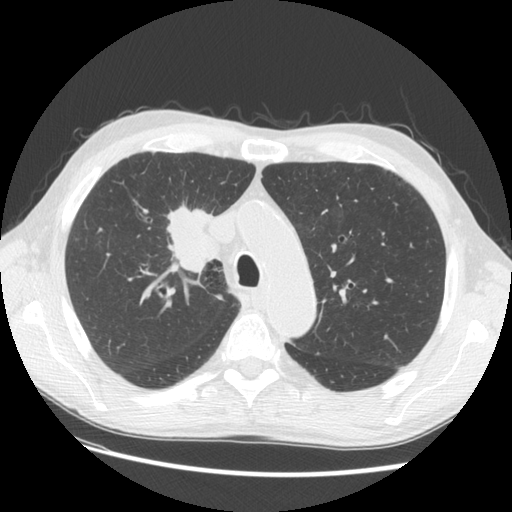
Axial slice from a low-dose chest CT screening exam; third screening round (two years after baseline); lung window (W 1500 / L -600 HU); 2.5 mm slice thickness; slice 37 of 133 in the series; 512 × 512 image matrix. Male, age 73 years at enrolment. Current smoker at enrolment.
Lesion marked by an expert reader, bounding box [x1, y1, x2, y2] px = [142, 183, 233, 278]. The screening reader recorded 4 non-calcified nodules or masses ≥4 mm on this exam (right upper lobe, right upper lobe, right upper lobe, left lower lobe); which of them this box marks is not recorded. Official screen result: positive, other. Later outcome: lung cancer diagnosed 48 days after this screen — squamous cell carcinoma, NOS, right upper lobe, poorly differentiated (G3), stage IIIB (AJCC 6th edition), 56 mm at pathology.